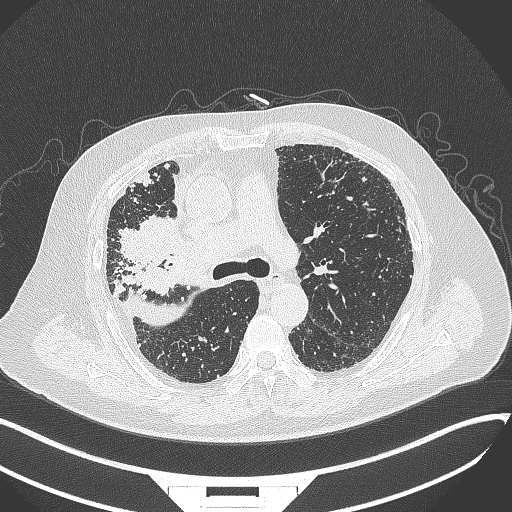
Chest CT, one axial slice; position 220 of 384 along the scan axis; lung window (W 1500 / L -600 HU); 512 × 512 image matrix, field of view 400 × 400 mm. Patient: male, 69 years. Case-level facts recorded for this patient, not image findings: clinical TNM (as recorded): T4 N3 M1.
Annotated regions visible in this slice (rectangle marked by the reading radiologist):
- lung tumour (recorded histology: adenocarcinoma): bounding box (x1, y1, x2, y2) in pixels: (118, 216, 186, 276)